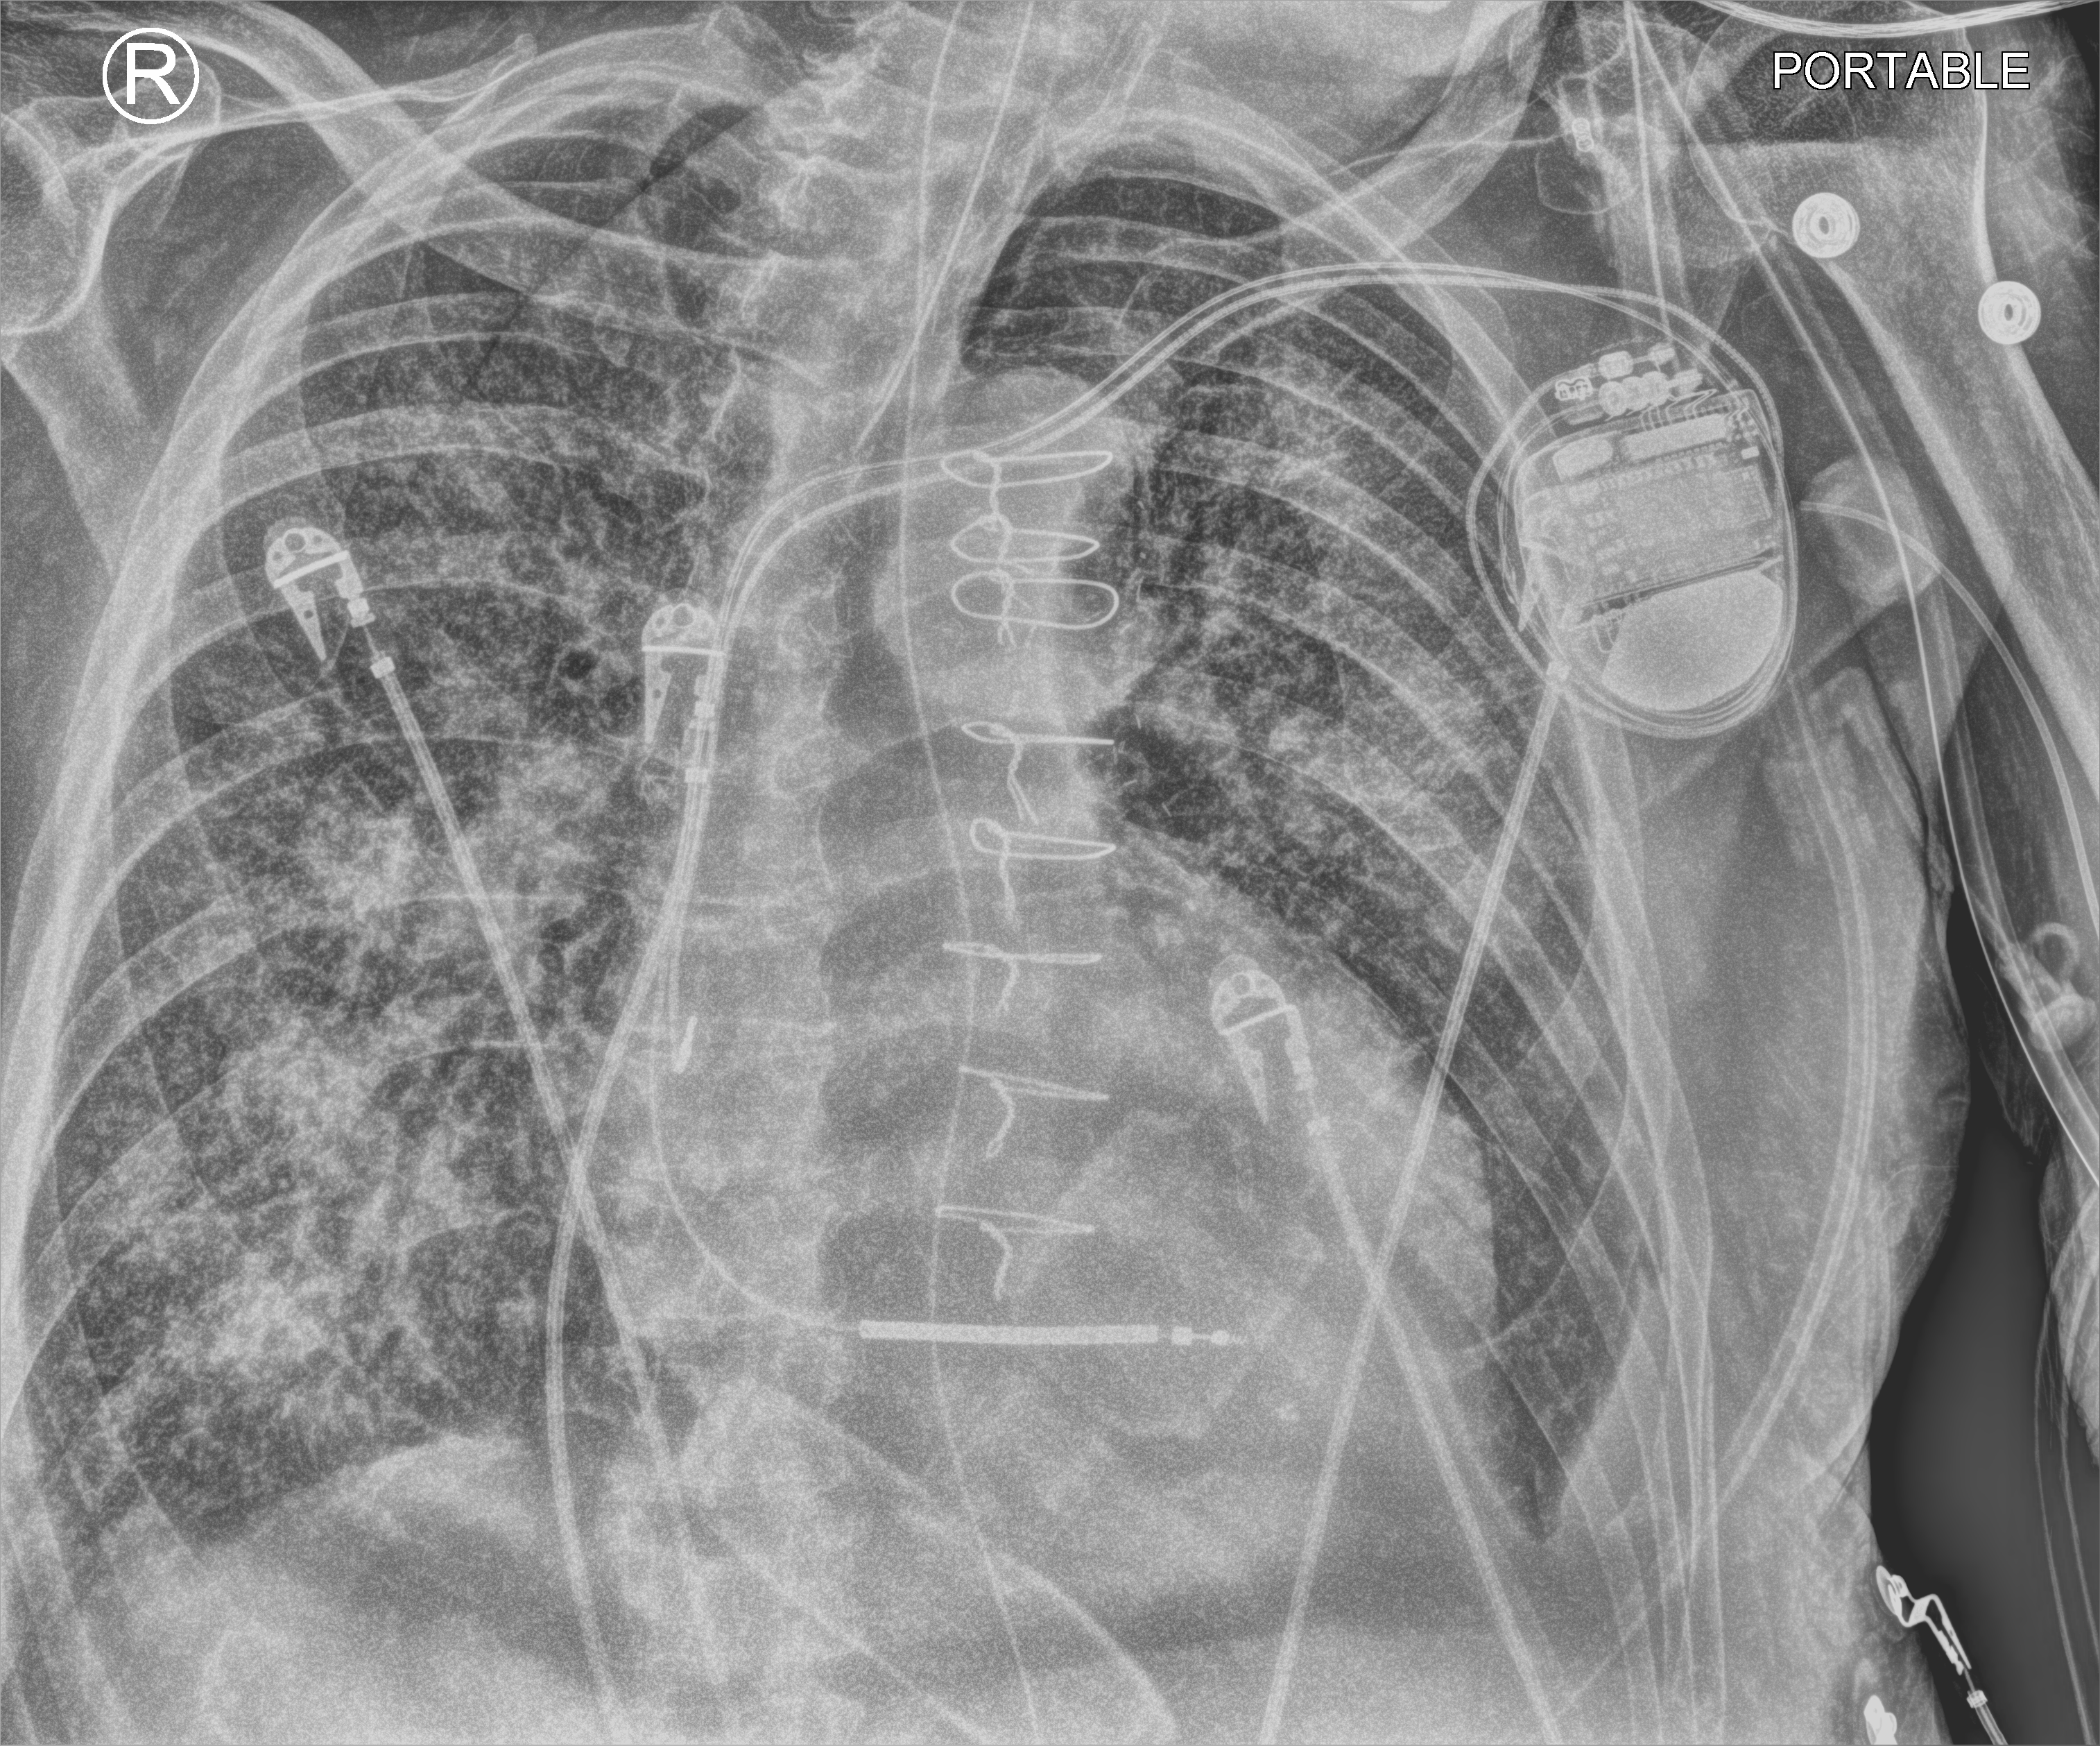
Chest X-ray (portable), anteroposterior (AP) projection. Male patient hospitalised with COVID-19, age 75–90 years.
From the hospital-stay record, not from the radiograph (when in the stay this image was taken is not recorded): length of hospital stay: 11 days; mechanically ventilated during this hospital stay: yes.